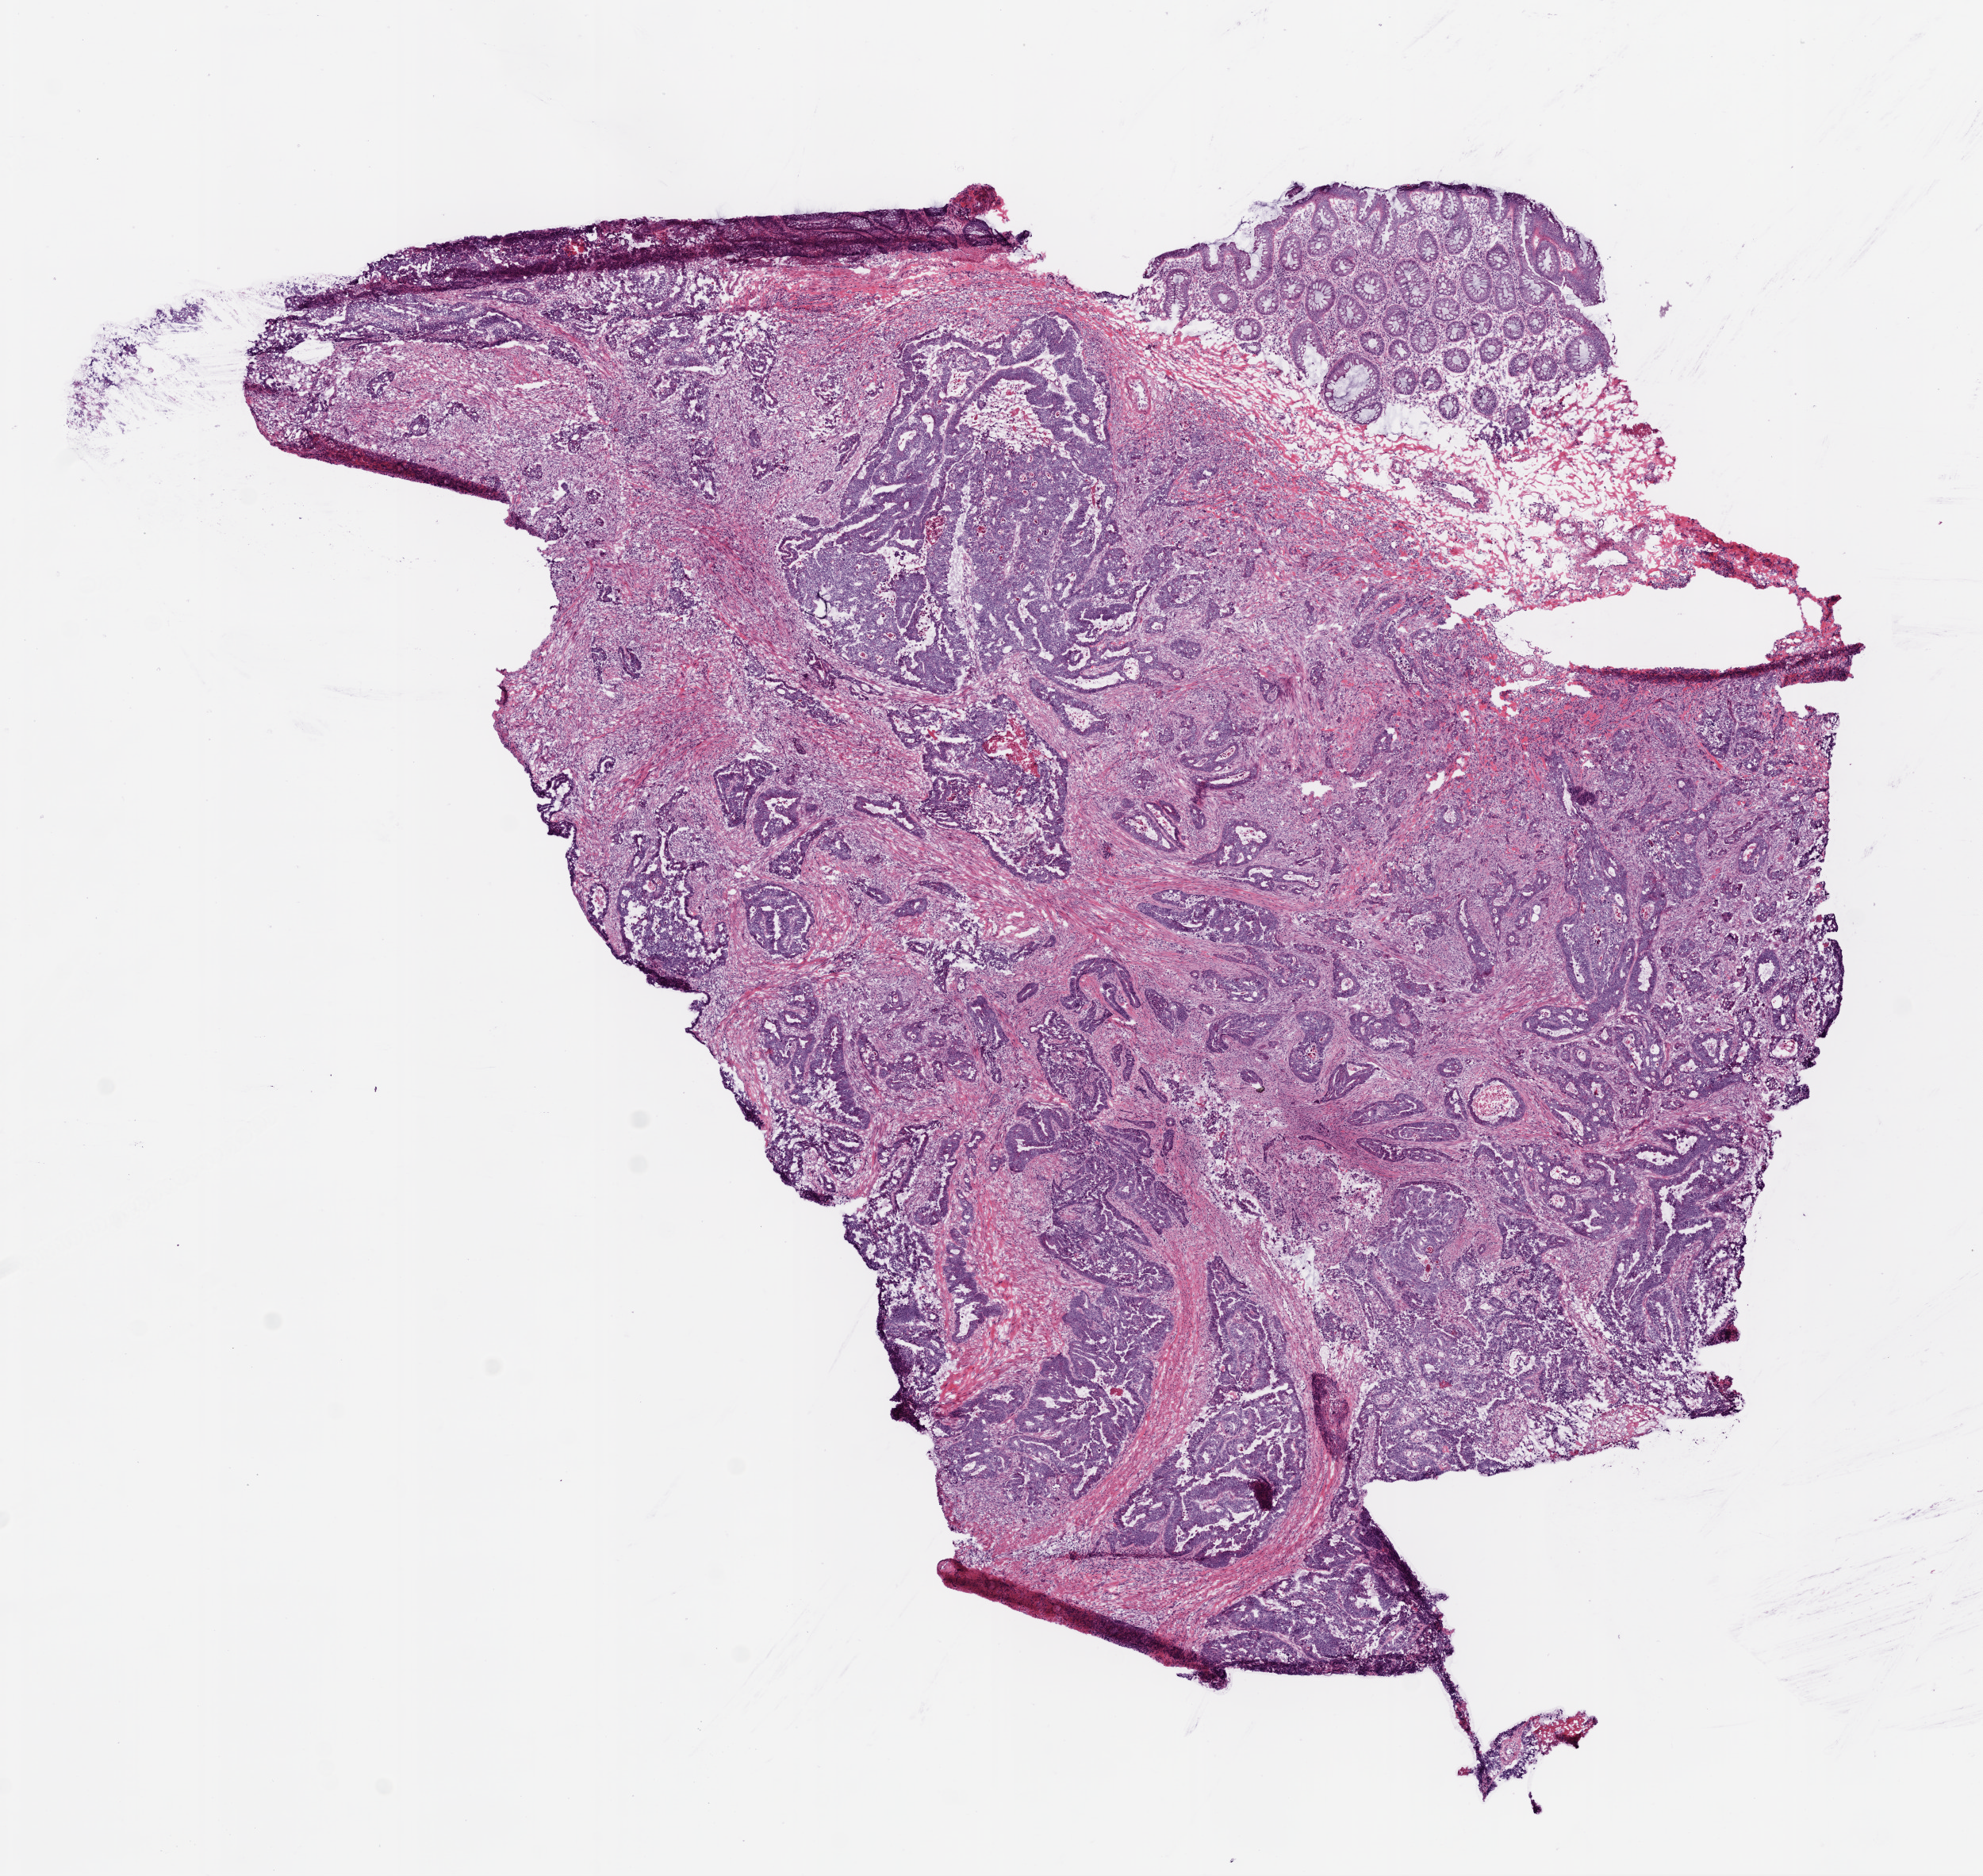
Digitized H&E-stained tissue section (whole slide) — low-resolution overview of the scanned area, about 10.0 x 9.5 mm (acquisition: 20x scan); frozen section from the top of the tissue portion; sample: primary tumour, rectum. Male patient; age at initial diagnosis 63 years. Pathologist review of this section (percent, as recorded): tumour cells 62%, tumour nuclei 75%, normal cells 15%, stromal cells 20%, necrosis 3%.
* AJCC pathologic stage: IIA (6th edition)
* histologic diagnosis: Adenocarcinoma, NOS (colon, NOS)
* TNM: T3 N0 M0
* lymph nodes positive (case pathology): 0 of 15 examined